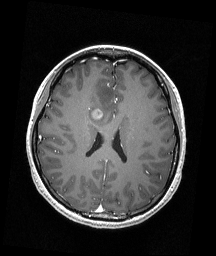
Brain MRI from a brain-tumour surgery series, one axial slice. Slice 77 of 192 in the series (ordered by position). T1-weighted post-contrast. 216 × 256 image matrix, field of view 211 × 250 mm. From the clinical record (not read from this slice): histopathology: Astrocytoma; WHO grade: 4; IDH mutation: yes.
Structures marked on this image (outlined manually by an expert reader):
- tumour: bounding box (x1, y1, x2, y2) in pixels: (92, 110, 102, 118)